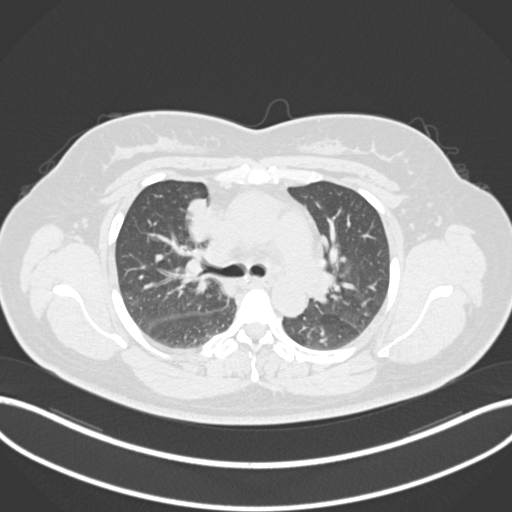
Chest CT, one axial slice. Reconstruction kernel B30f. 120 kVp. Lung window (W 1500 / L -600 HU). 1 mm slice thickness. 512 × 512 image matrix, field of view 400 × 400 mm. Patient: female, 46 years. From the clinical record (not read from this slice): clinical TNM (as recorded): T2a N1 M0.
Structures marked on this image (rectangle marked by the reading radiologist):
- lung tumour (recorded histology: adenocarcinoma): box from (x=182, y=196) to (x=215, y=246) px